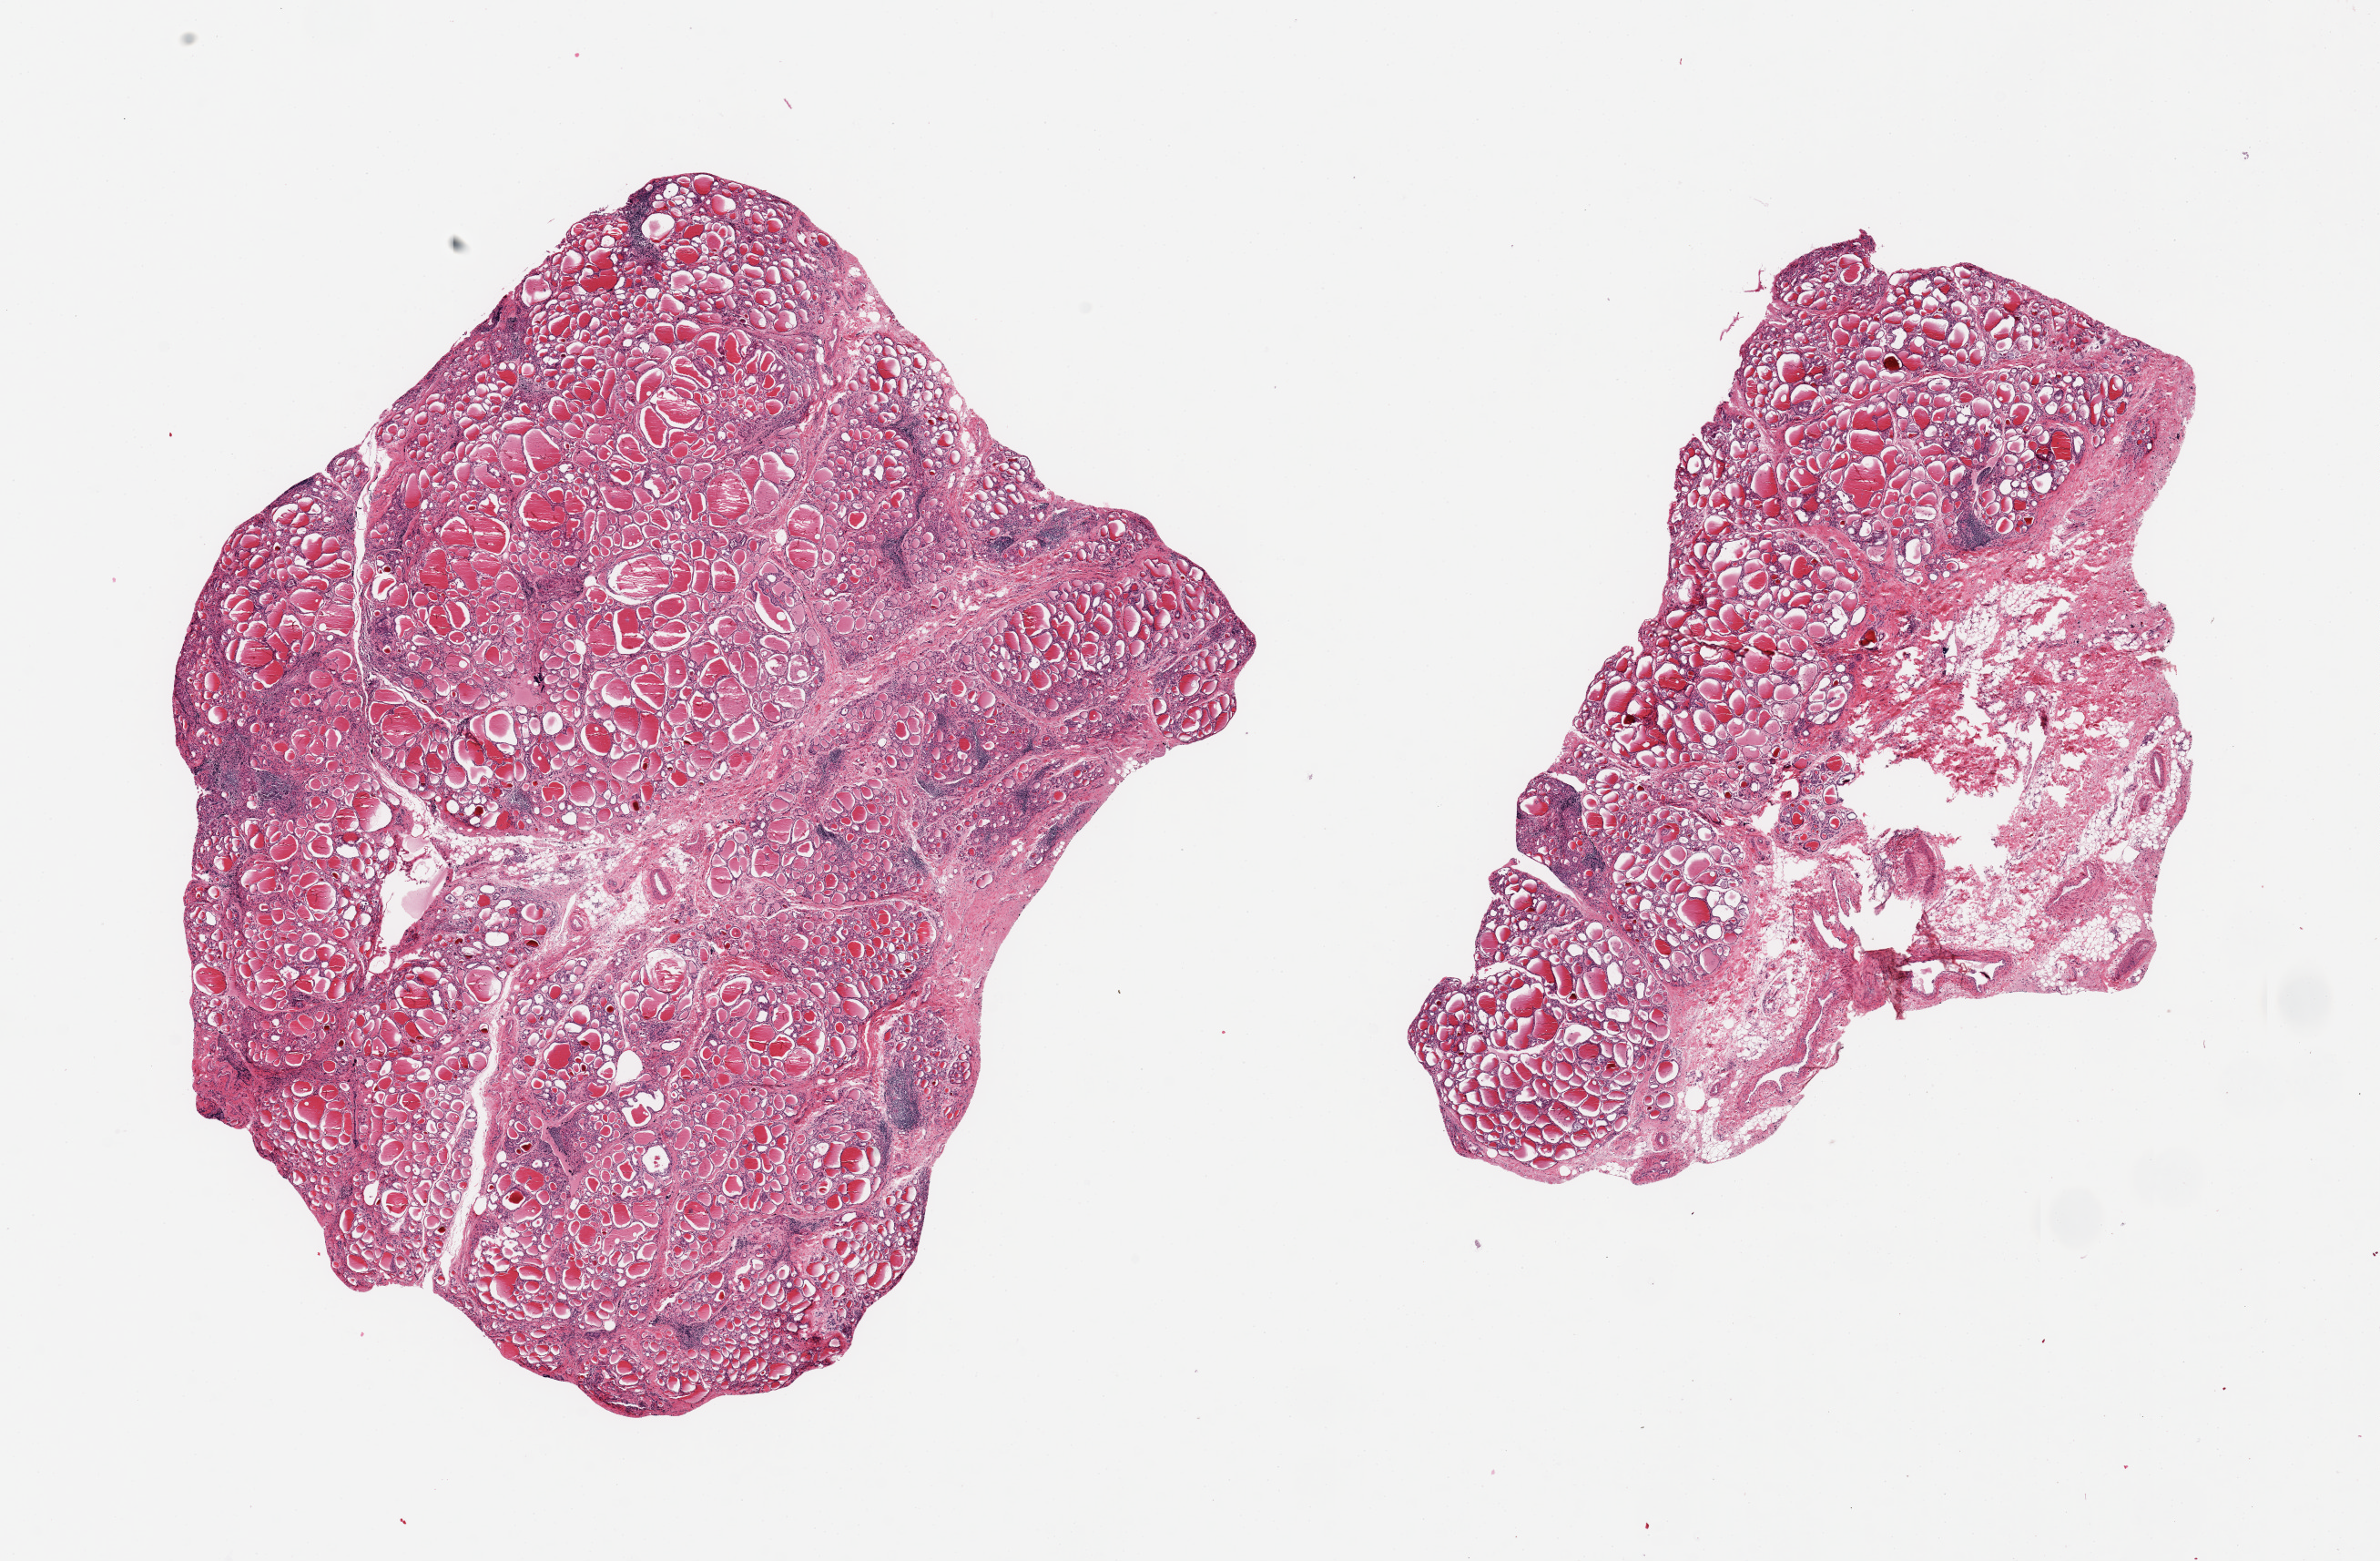
Whole-slide image, H&E stain, brightfield — low-resolution overview of the scanned area, about 20.7 x 13.6 mm, PAXgene-fixed, paraffin-embedded tissue, section of thyroid (target tissue), donor tissue sample. Donor sex: female.
Pathologist's review note for this sample: 2 pieces; interstitial fibrosis and micronodularity with scattered lymphocytic aggregates likely Hashimoto's thyroiditis, 1 piece is ~ 40% fat/fibrous/vessels.